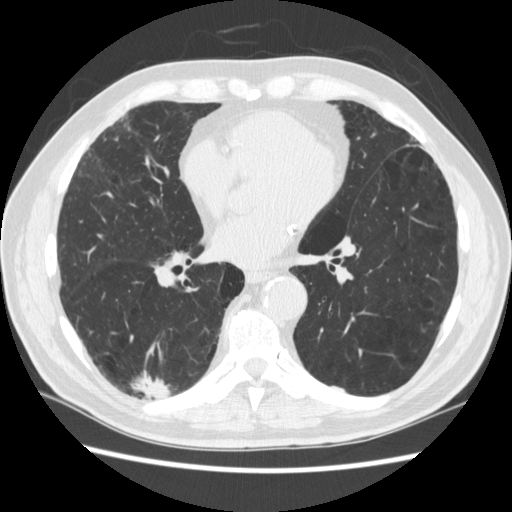
Low-dose screening chest CT, axial slice; third annual screen; lung window (W 1500 / L -600 HU); 1.25 mm slice thickness; slice 147 of 266 in the series. Male, age 70 years at enrolment. Former smoker at enrolment.
• Expert reader's lesion annotation, bounding box <123,360,183,418> (left, top, right, bottom; pixels).
• The screening reader recorded 4 non-calcified nodules or masses ≥4 mm on this exam (right lower lobe, right lower lobe, left lower lobe, left lower lobe); which of them this box marks is not recorded.
• Official screen result: positive, other.